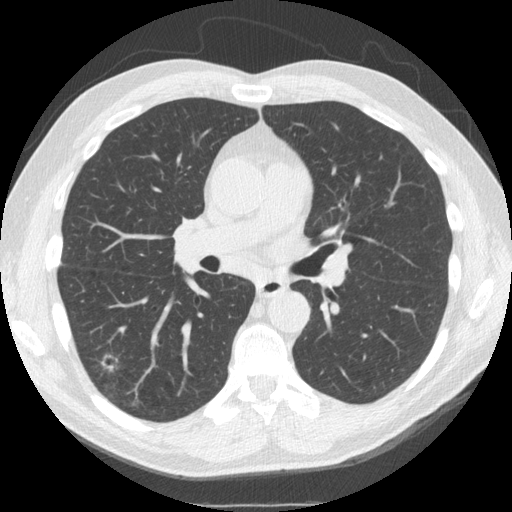
Low-dose screening chest CT, one axial slice; position 91 of 162 along the scan axis; lung window (W 1500 / L -600 HU); 512 × 512 image matrix, field of view 360 × 360 mm.
Annotated regions visible in this slice (expert manual segmentation):
- lesion 1 (nodule, lower lobe of right lung): bounding box [x1, y1, x2, y2] px = [101, 354, 118, 372]